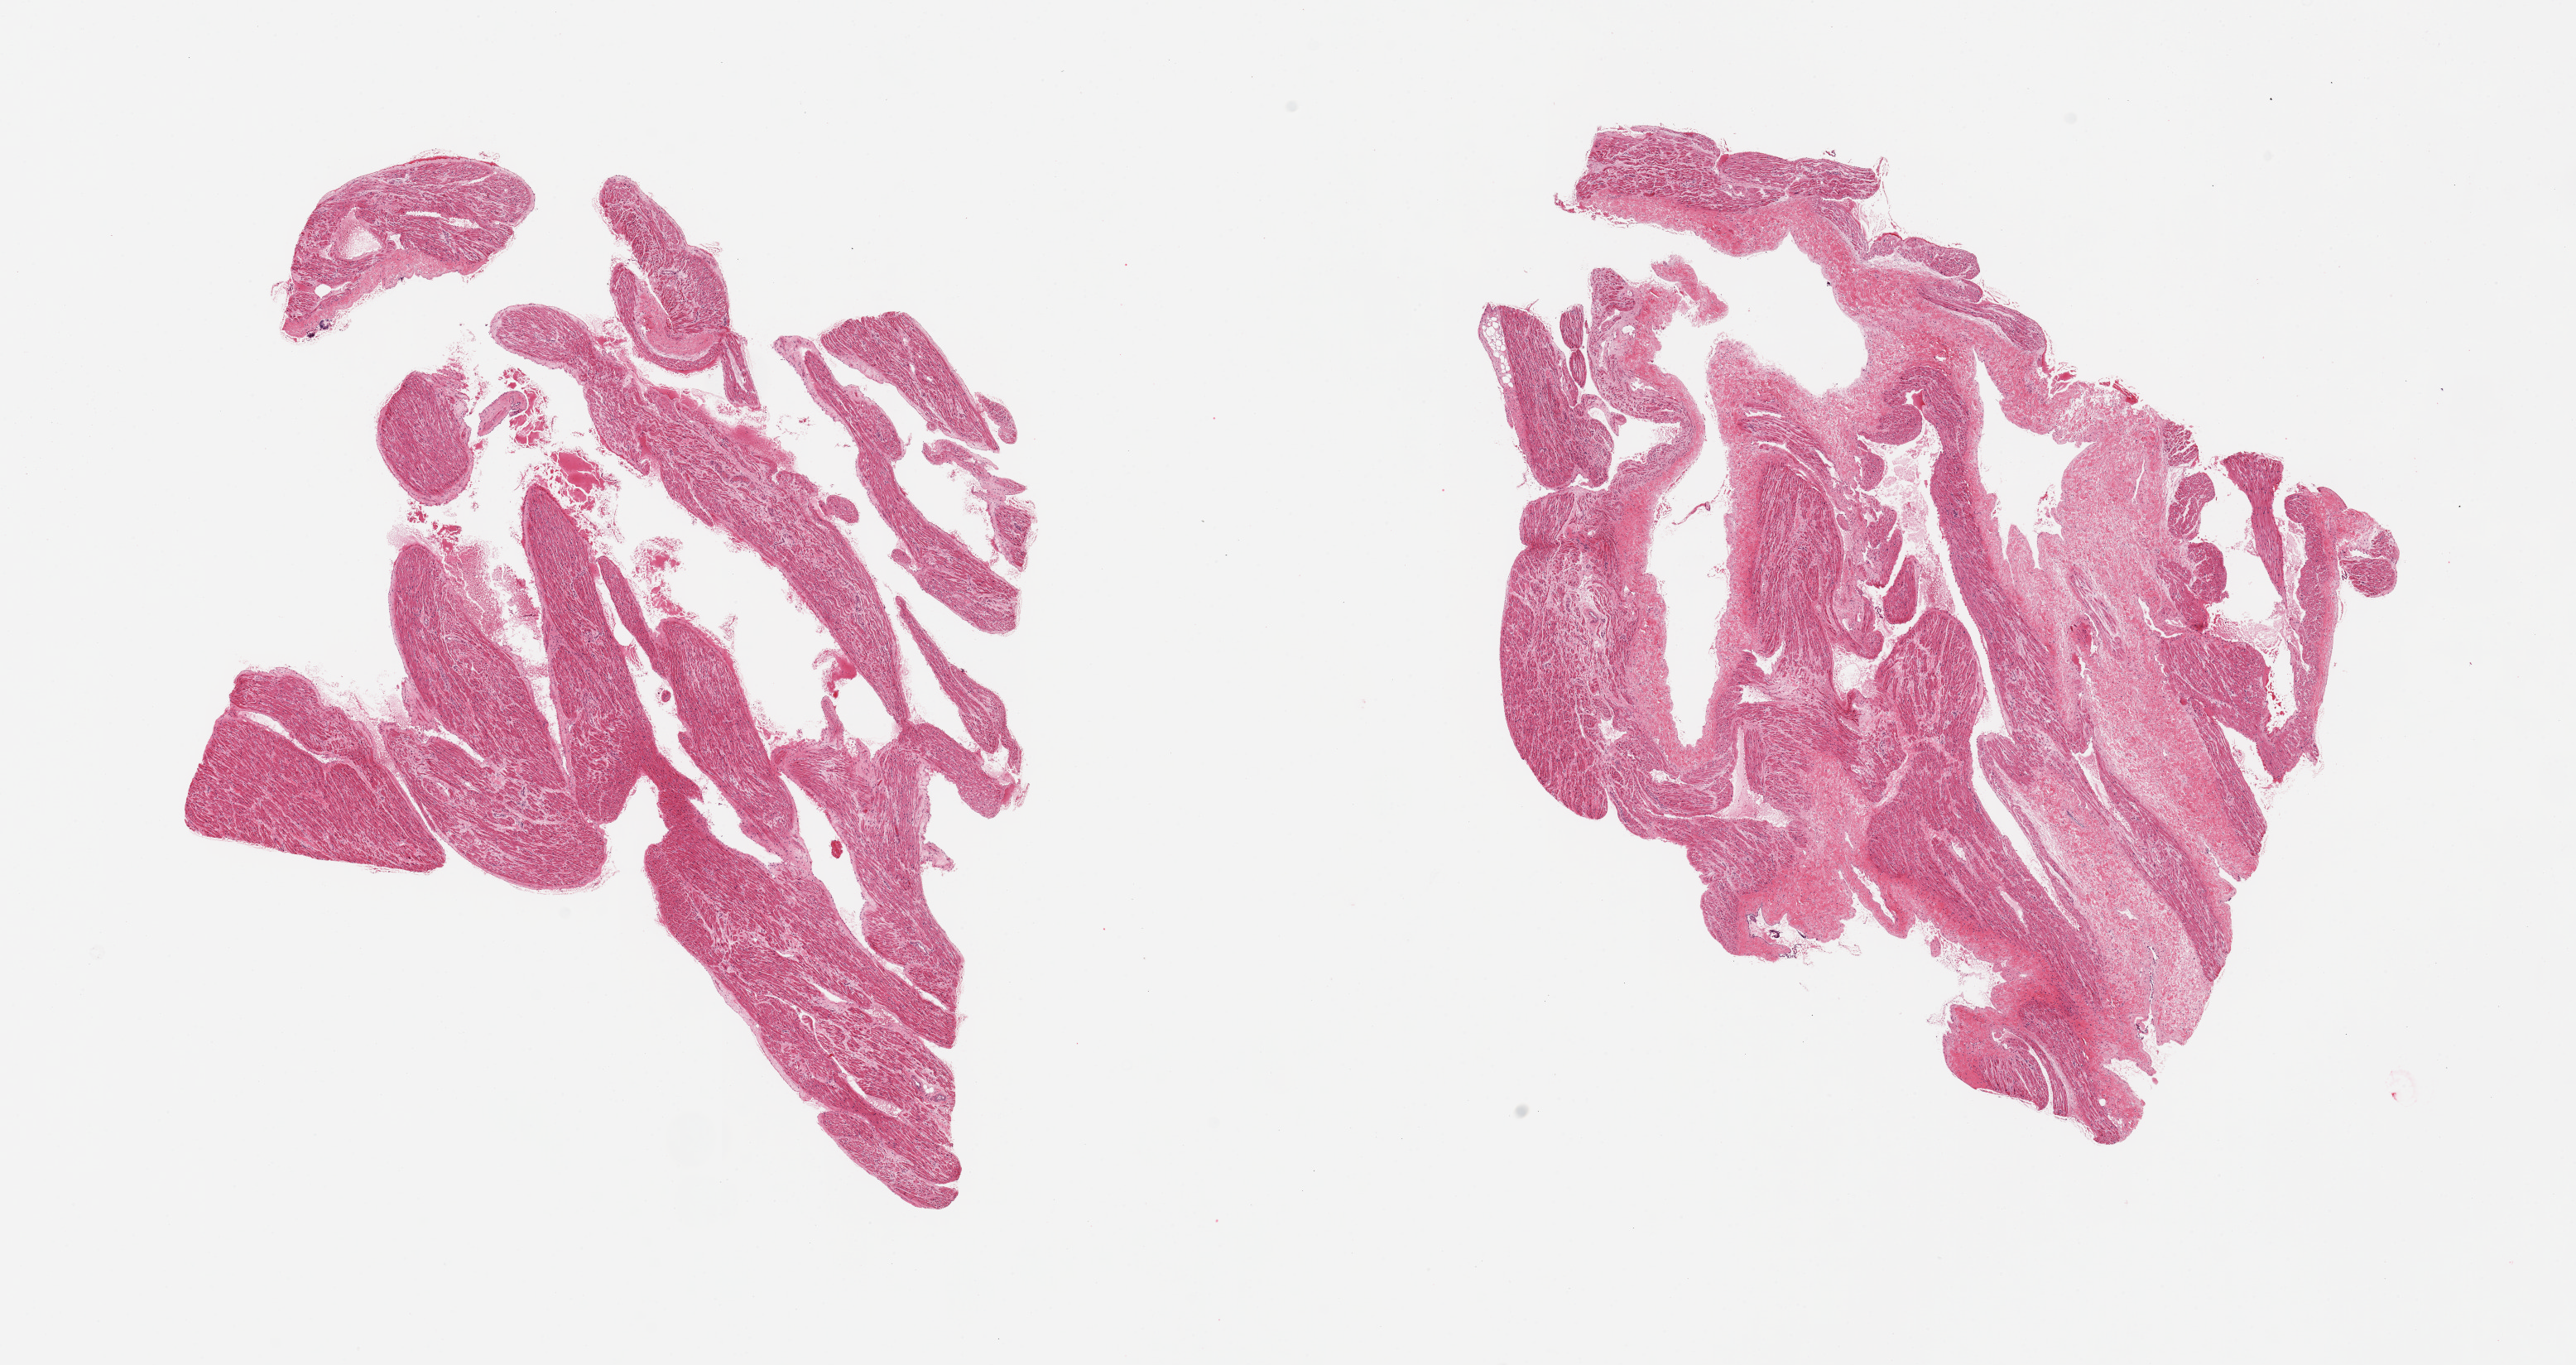
Digitized haematoxylin and eosin-stained section, brightfield, whole scanned area (about 24.6 x 13.0 mm) shown as a low-resolution overview, PAXgene-fixed, paraffin-embedded tissue, sampled site (target tissue): auricular appendage, tissue donor sample. Male donor.
- review note (as recorded): 2 pieces; 1 piece has 30% fibrous stroma